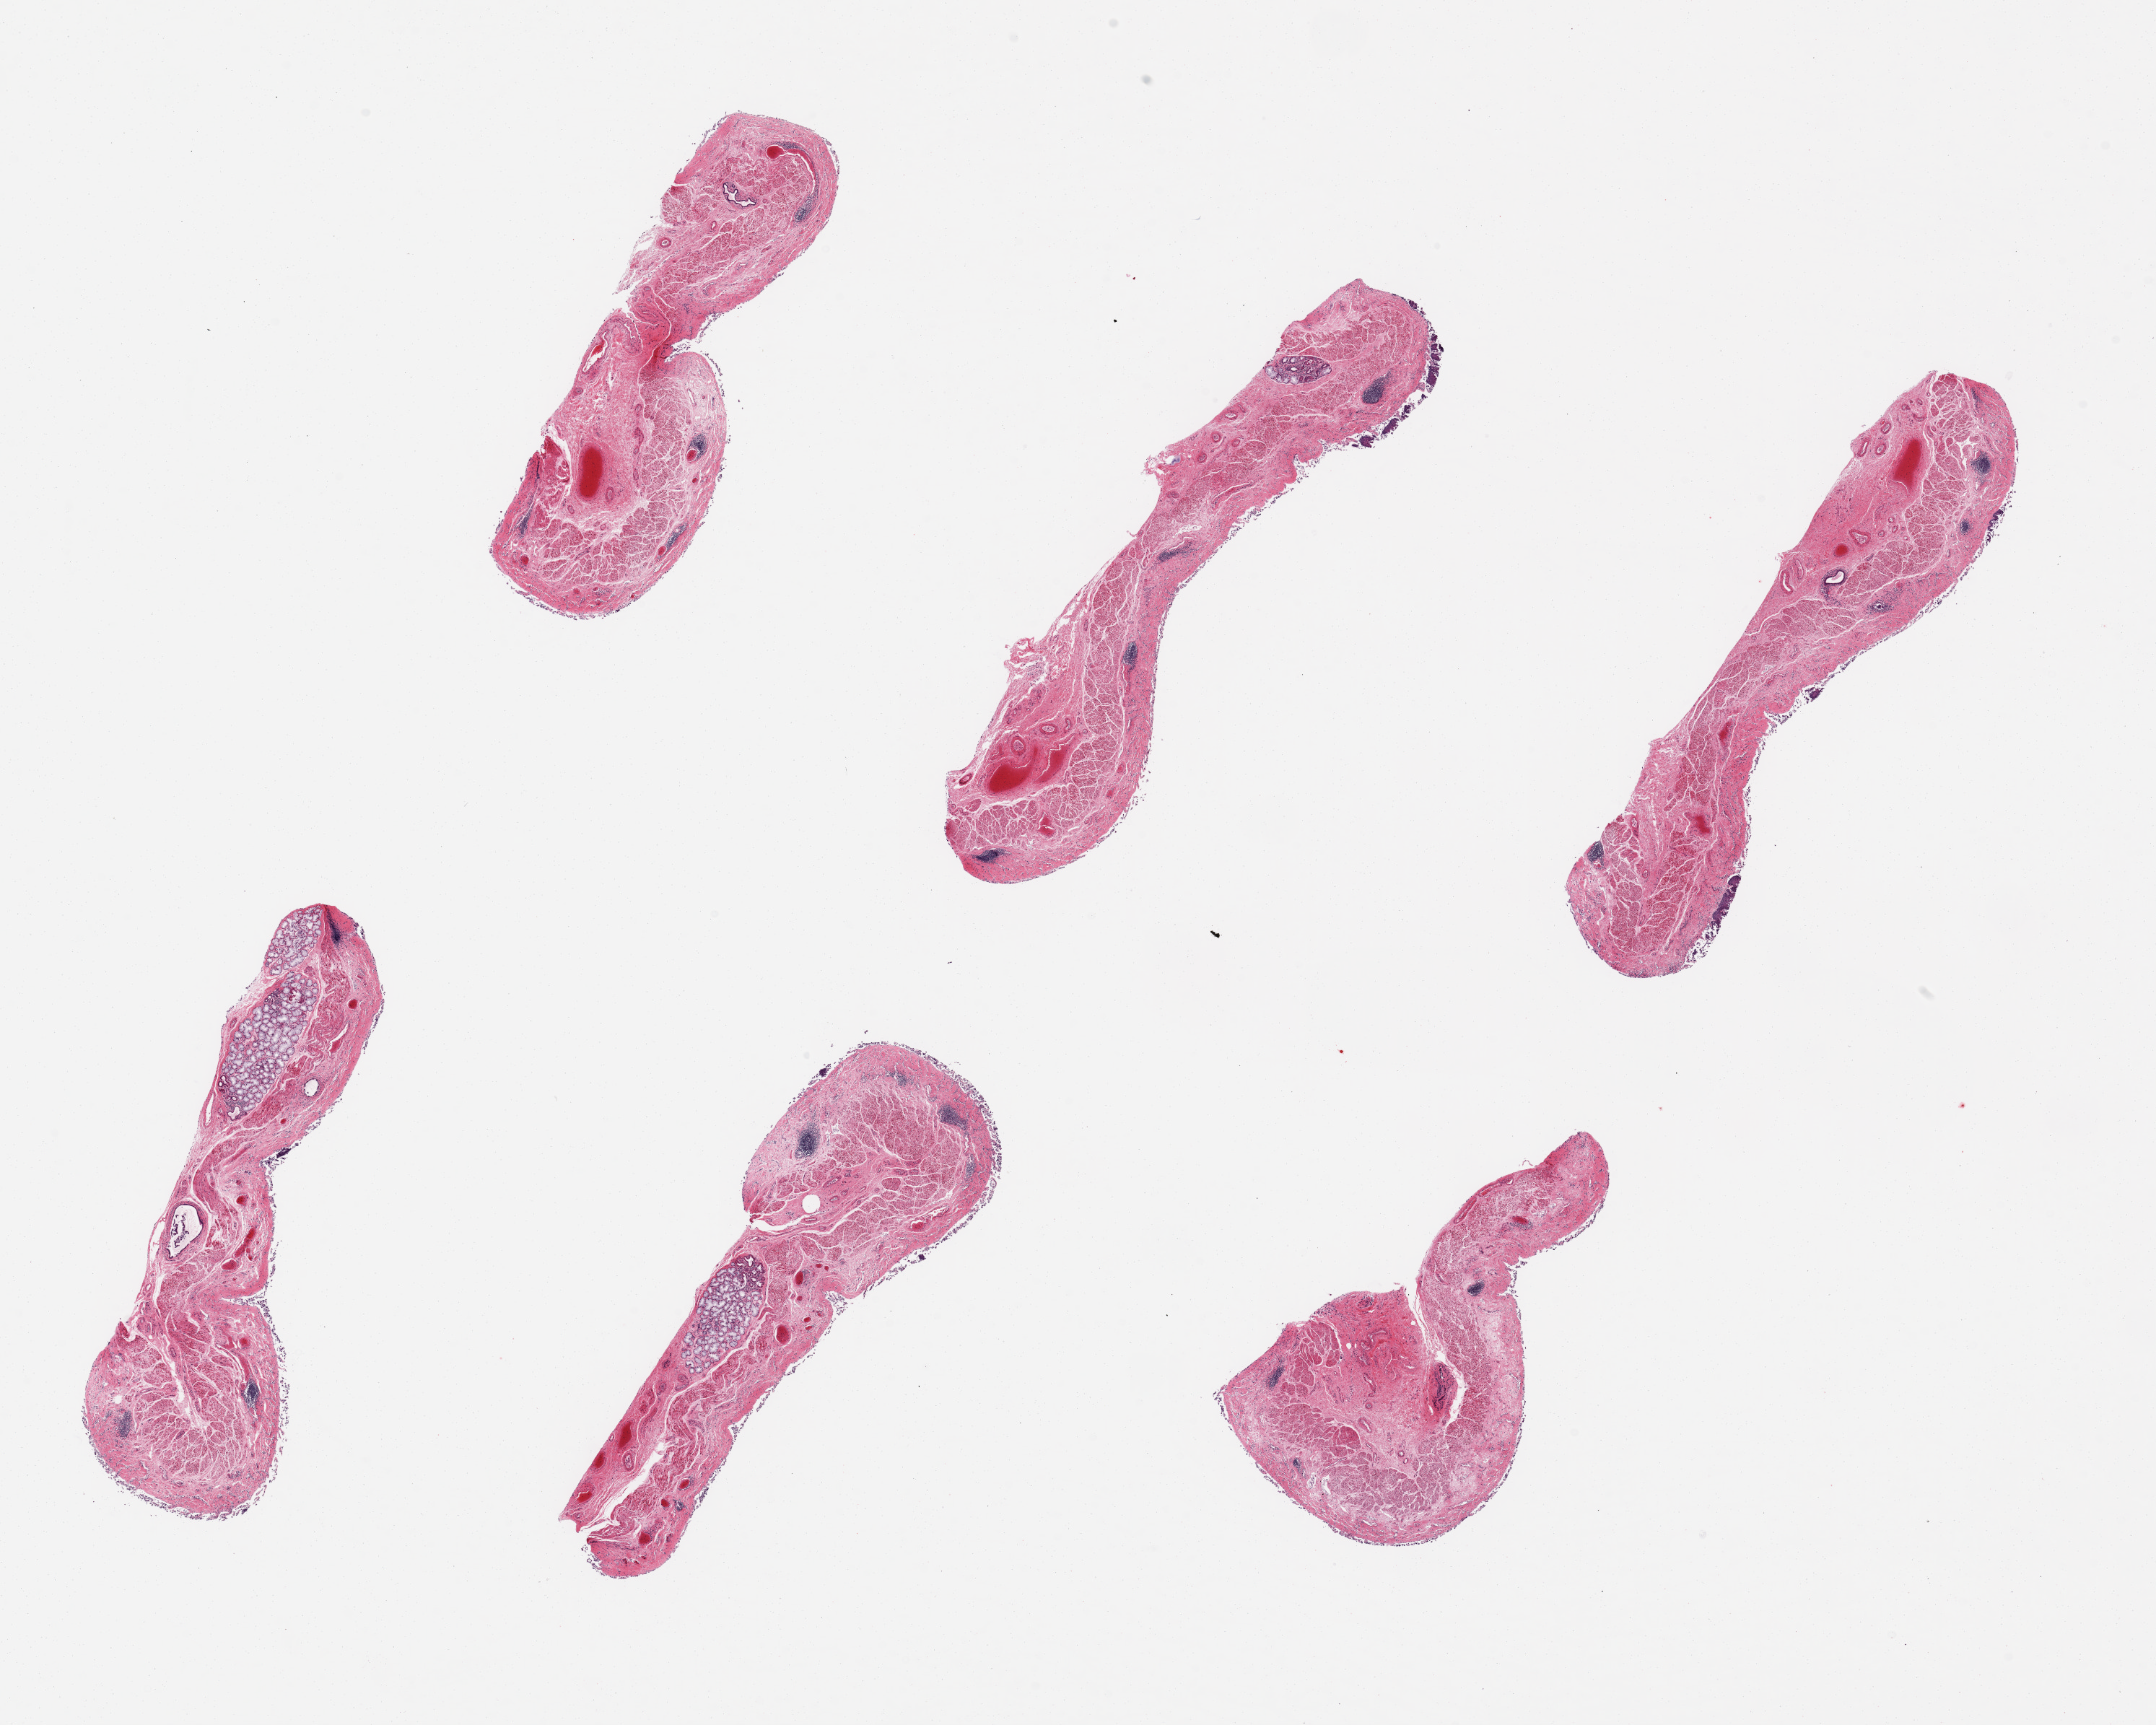
Whole-slide image, H&E stain — a low-resolution overview of the entire scanned area, about 23.6 x 18.9 mm; PAXgene-fixed, paraffin-embedded tissue; section of esophageal mucous membrane (target tissue); tissue donor sample. Donor sex: male.
Reviewer comment on this tissue sample: 6 pieces, 8x2mm; Mucosa totally slough save for a few minute foci, badly preserved; Prominent sub mucocal glands.